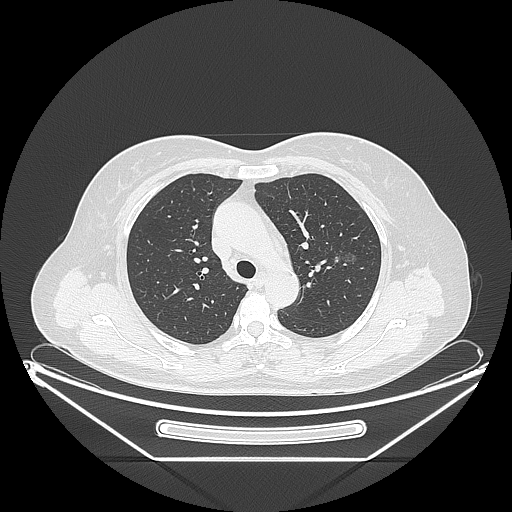
Chest CT, one axial slice; position 151 of 226 along the scan axis; 120 kVp; lung window (W 1500 / L -600 HU); 1.25 mm slice thickness; 512 × 512 image matrix. Female patient, age 54 years. Case-level facts recorded for this patient, not image findings: clinical TNM (as recorded): T1c N0 M0; histopathological grade: G1.
Outlined on this slice (bounding box drawn by a radiologist):
- lung tumour (recorded histology: adenocarcinoma): bounding box <332,243,367,270> (left, top, right, bottom; pixels)